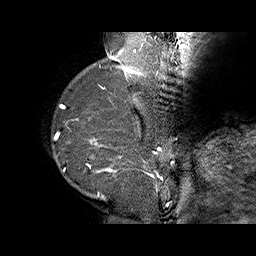
Breast MRI (dynamic contrast-enhanced), one sagittal slice. Dynamic contrast-enhanced series, time point 2 of 6 at this slice position (early post-contrast). 1.5 T. TE 4.5 ms, TR 32.4 ms. 3 mm slice thickness. 256 × 256 image matrix, field of view 180 × 180 mm. Female patient. Case-level facts recorded for this patient, not image findings: setting: breast cancer imaged before/during neoadjuvant chemotherapy; receptor status: HR-positive, HER2-negative.
Annotated regions visible in this slice (semi-automatically segmented with operator editing):
- analysis volume of interest (the breast-tissue region the enhancement analysis was run in; not a lesion): bounding box (x1, y1, x2, y2) in pixels: (71, 128, 159, 202)
- tumour enhancement mask (voxels above the 100 % enhancement threshold inside the analysis volume of interest): (87, 137, 159, 188)